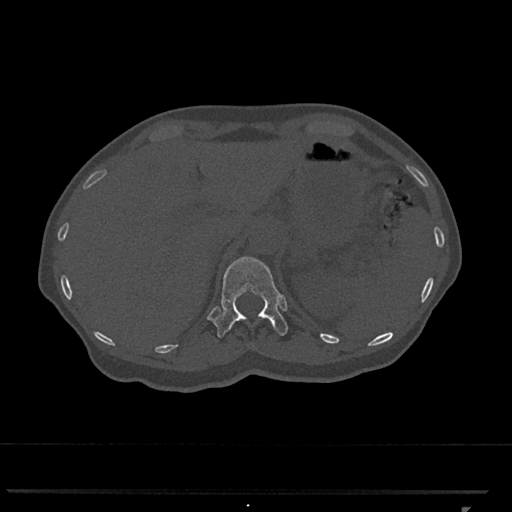
CT including the spine, one axial slice; position 471 of 793 along the scan axis; reconstruction kernel Br40s/3; 120 kVp; bone window (W 1800 / L 400 HU); 0.5 mm slice thickness; 512 × 512 image matrix, field of view 380 × 380 mm. Patient: female, 62 years. From the clinical record (not read from this slice): primary cancer: renal.
Outlined on this slice (semi-automatic segmentation, software-assisted and operator-edited):
- T12 vertebra: bounding box <214,256,288,338> (left, top, right, bottom; pixels)